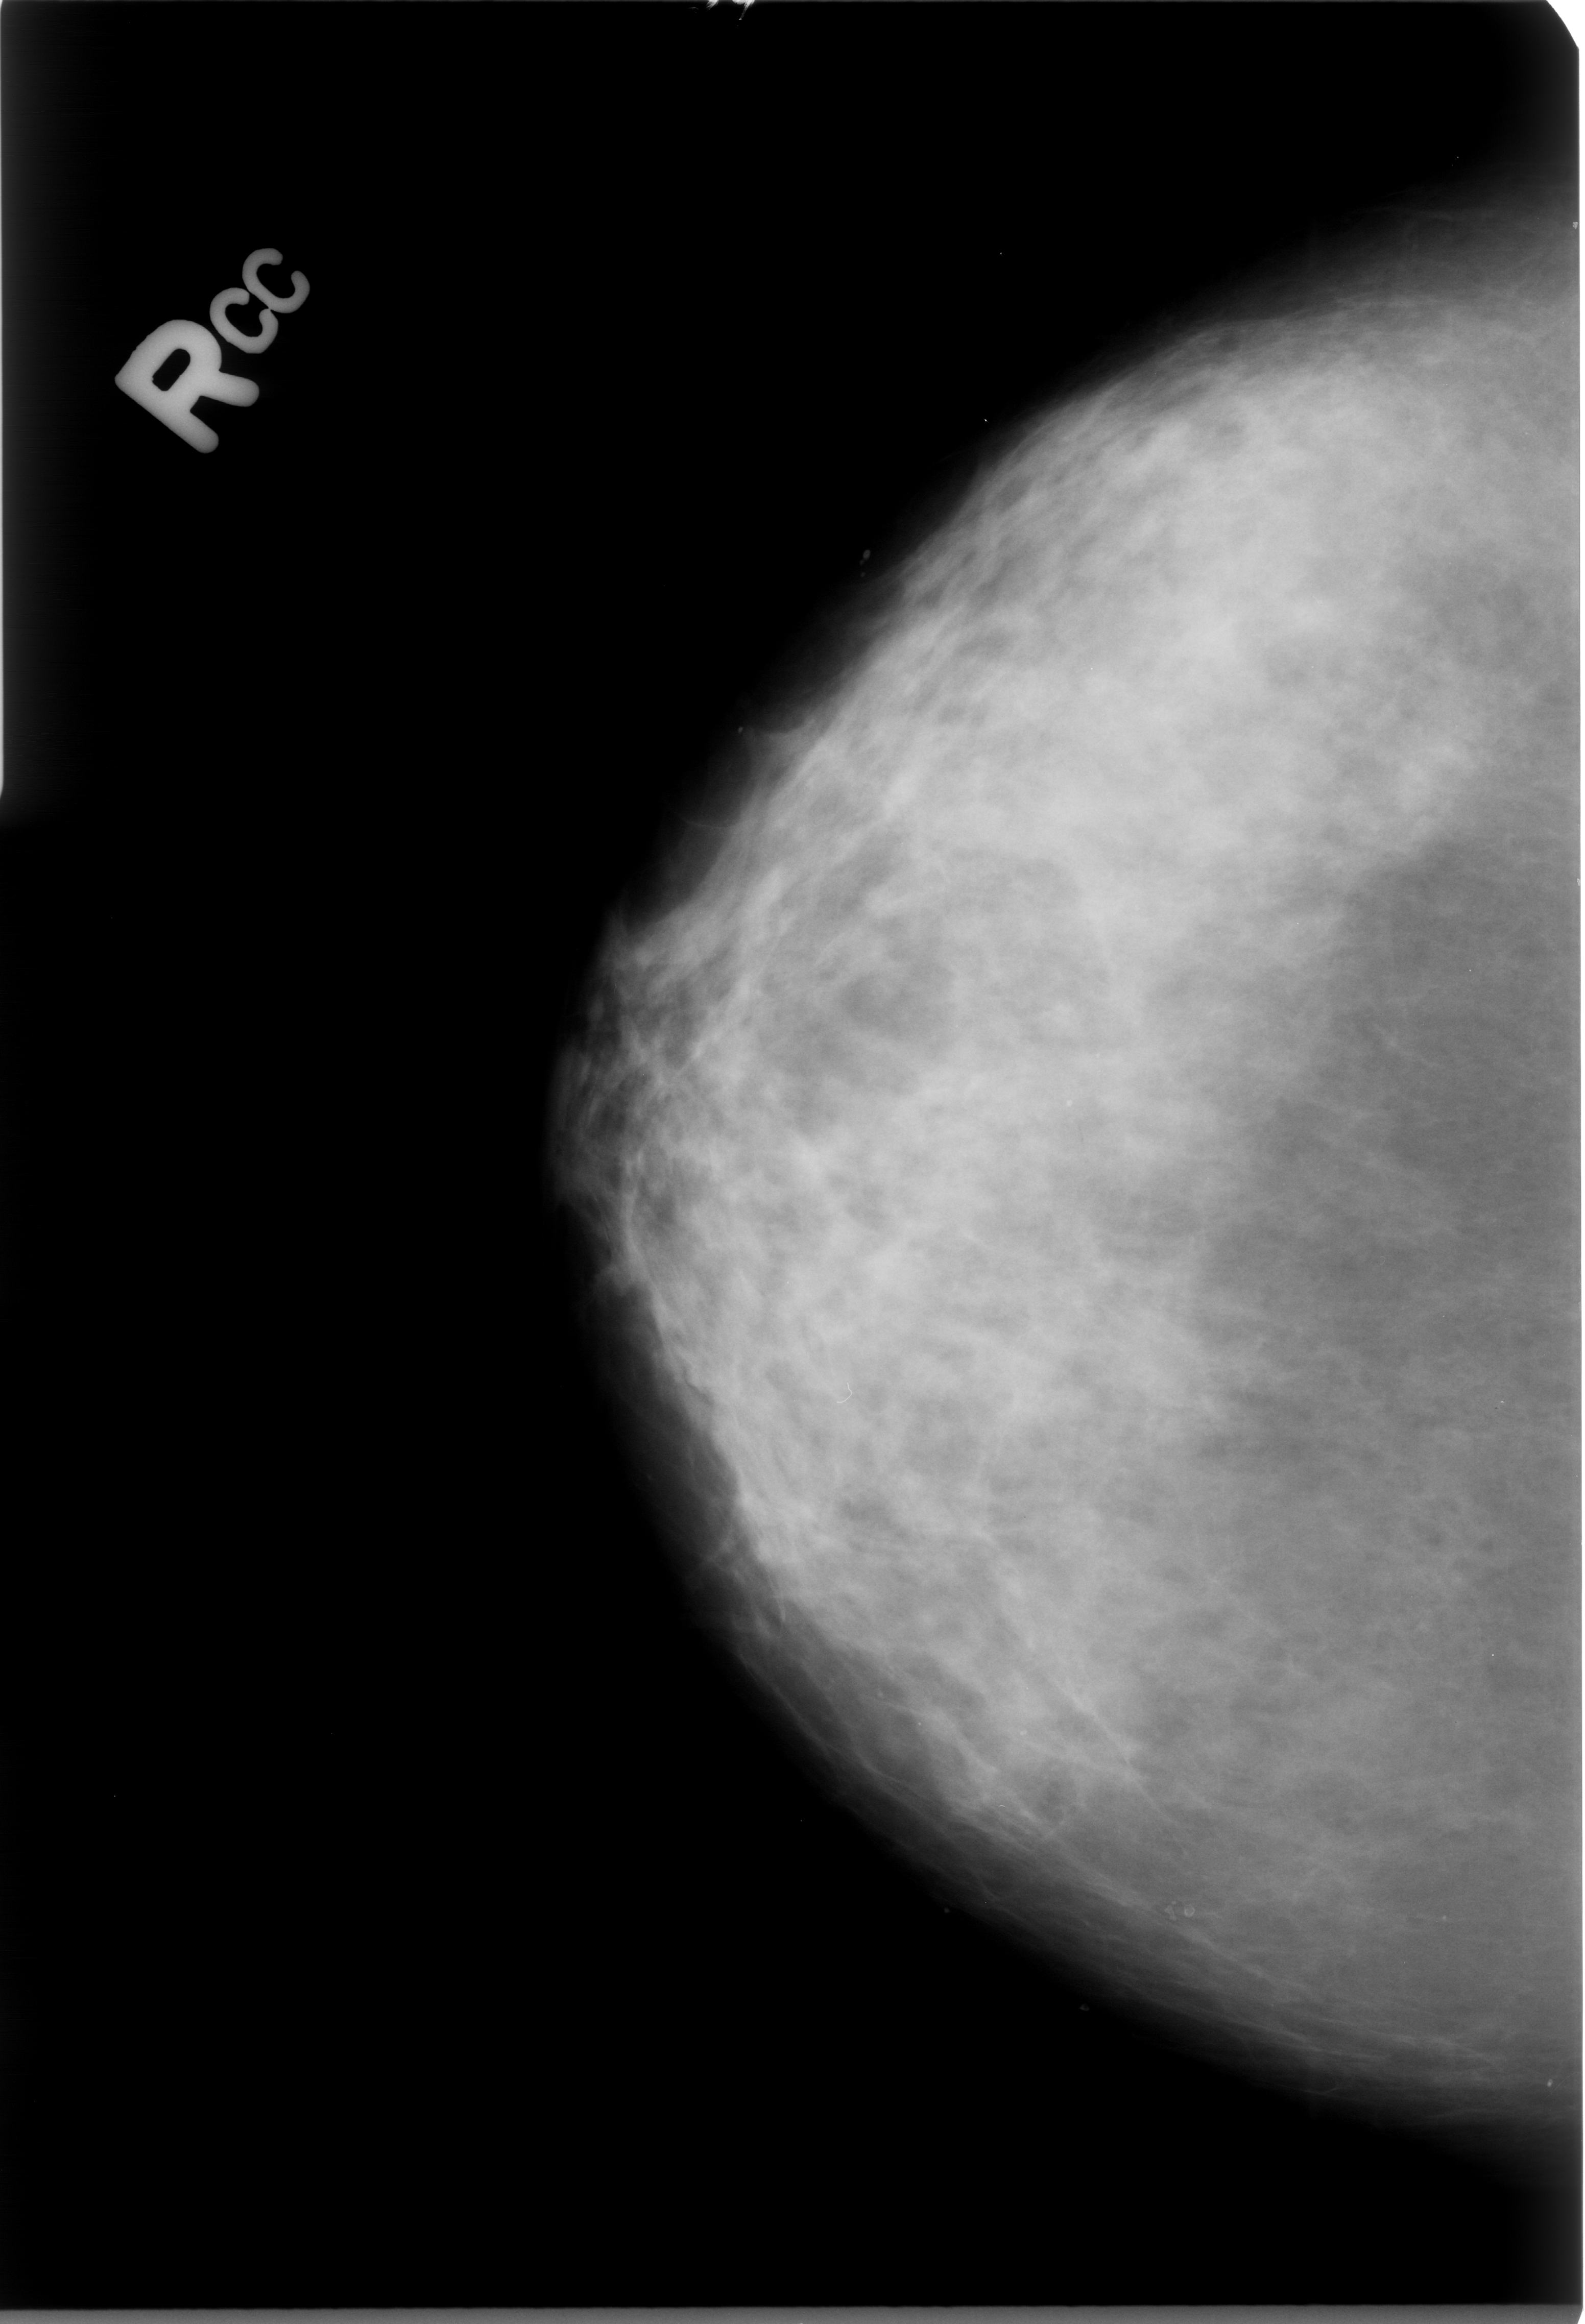
Mammogram (digitized film), right breast, craniocaudal (CC) view, BI-RADS breast density category 3 (scale 1–4).
- Abnormality record for this image: Finding 1 of 2: calcifications, morphology round and regular / lucent centered; BI-RADS assessment category 2; benign; no additional work-up was recommended (benign without callback).
- Finding 2 of 2: calcifications, morphology round and regular / lucent centered; BI-RADS assessment category 2; benign; no additional work-up was recommended (benign without callback).